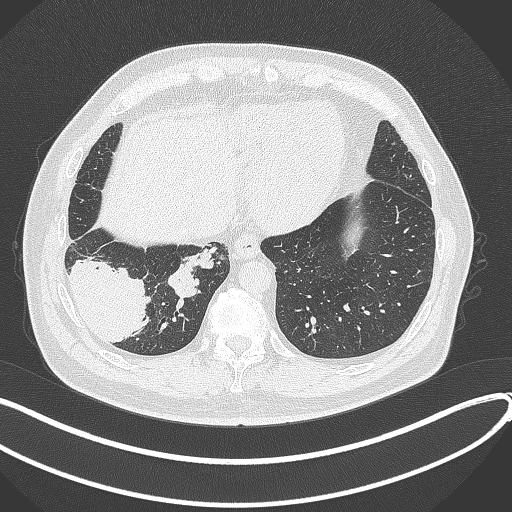
Chest CT, one axial slice. Slice 81 of 360 in the series (ordered by position). Lung window (W 1500 / L -600 HU). 512 × 512 image matrix. Male patient, age 59 years.
Outlined on this slice (rectangle marked by the reading radiologist):
- lung tumour (recorded histology: adenocarcinoma): box from (x=67, y=251) to (x=154, y=342) px